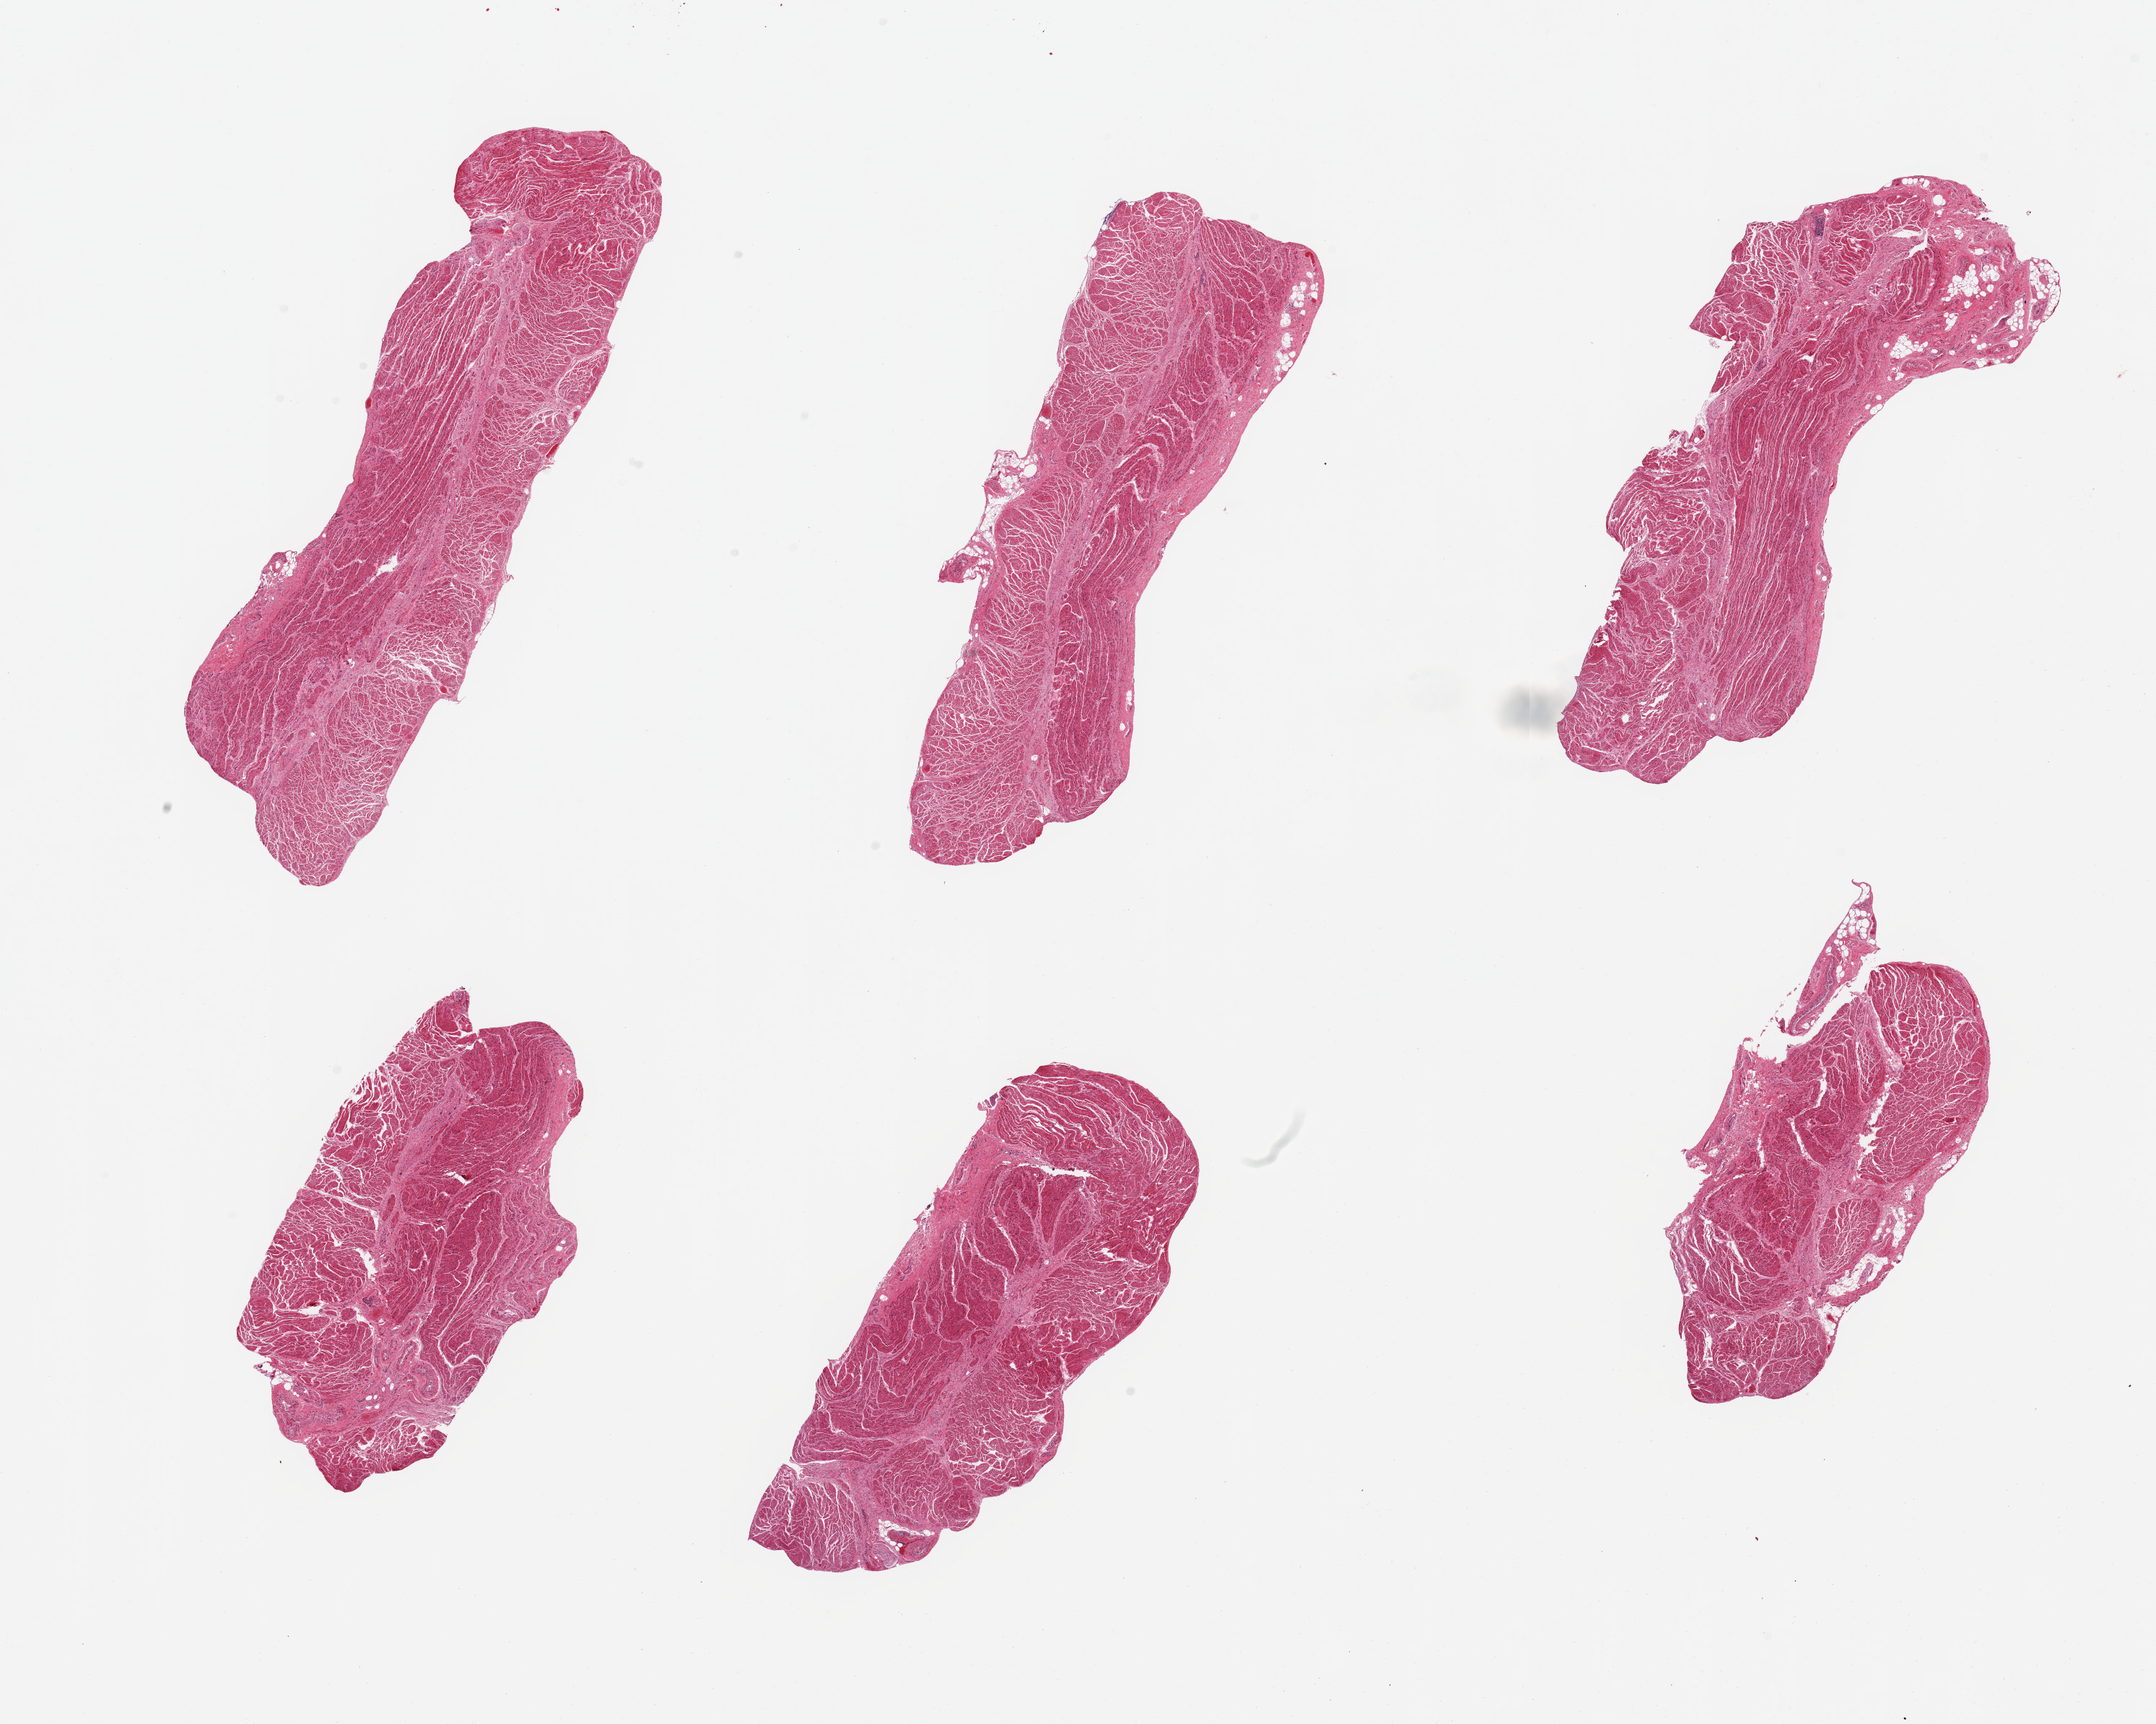
Digitized hematoxylin and eosin (H&E)-stained section, whole scanned area (about 23.6 x 18.9 mm) shown as a low-resolution overview. PAXgene-fixed, paraffin-embedded tissue. Section of gastroesophageal junction (target tissue). Tissue donor sample. Male donor.
Review note (as recorded): 6 pieces; well trimmed target muscularis.